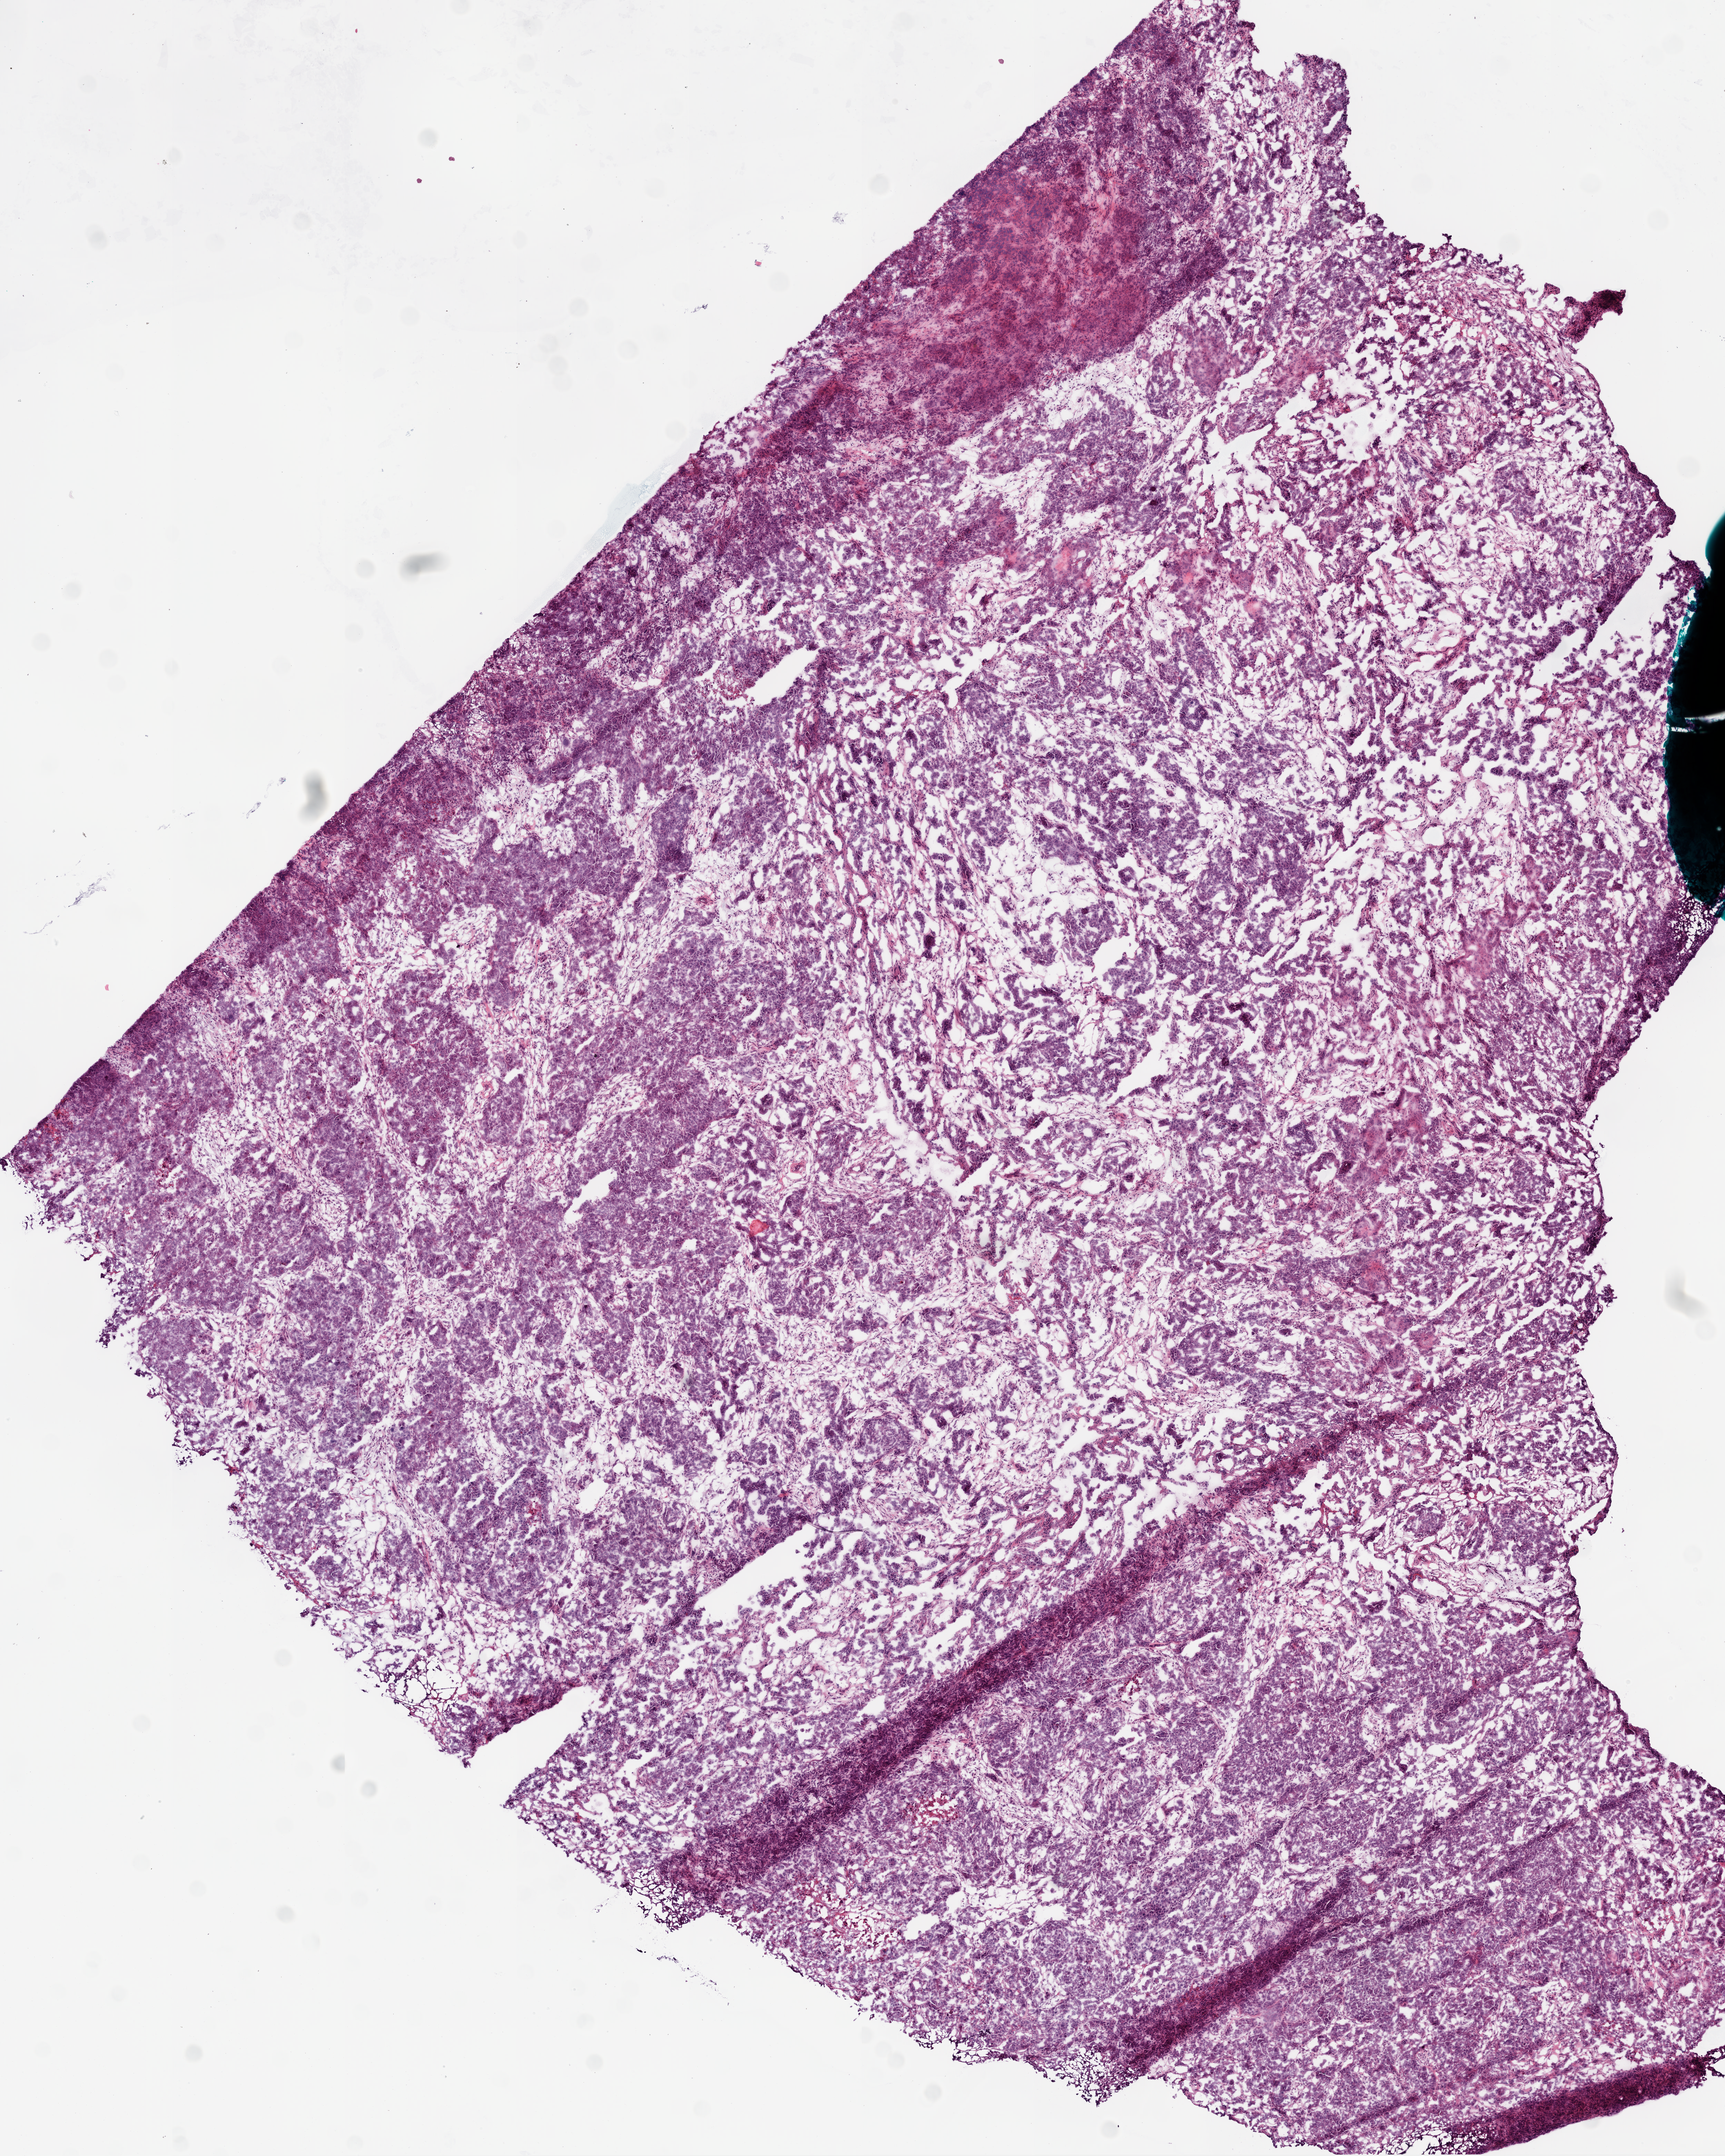
H&E-stained whole-slide image, low-resolution overview of the scanned area, about 10.0 x 12.5 mm (acquisition: 20x scan); frozen section; primary tumour sample from the ovary. Female patient; age at initial diagnosis 57 years. Histologic grade: G3 (poorly differentiated). Pathologist review of this section (percent, as recorded): tumour cells 89%, tumour nuclei 95%, normal cells 0%, stromal cells 5%, necrosis 1%.
Laterality: right. FIGO stage: IIIC. Diagnosis: Serous cystadenocarcinoma, NOS.